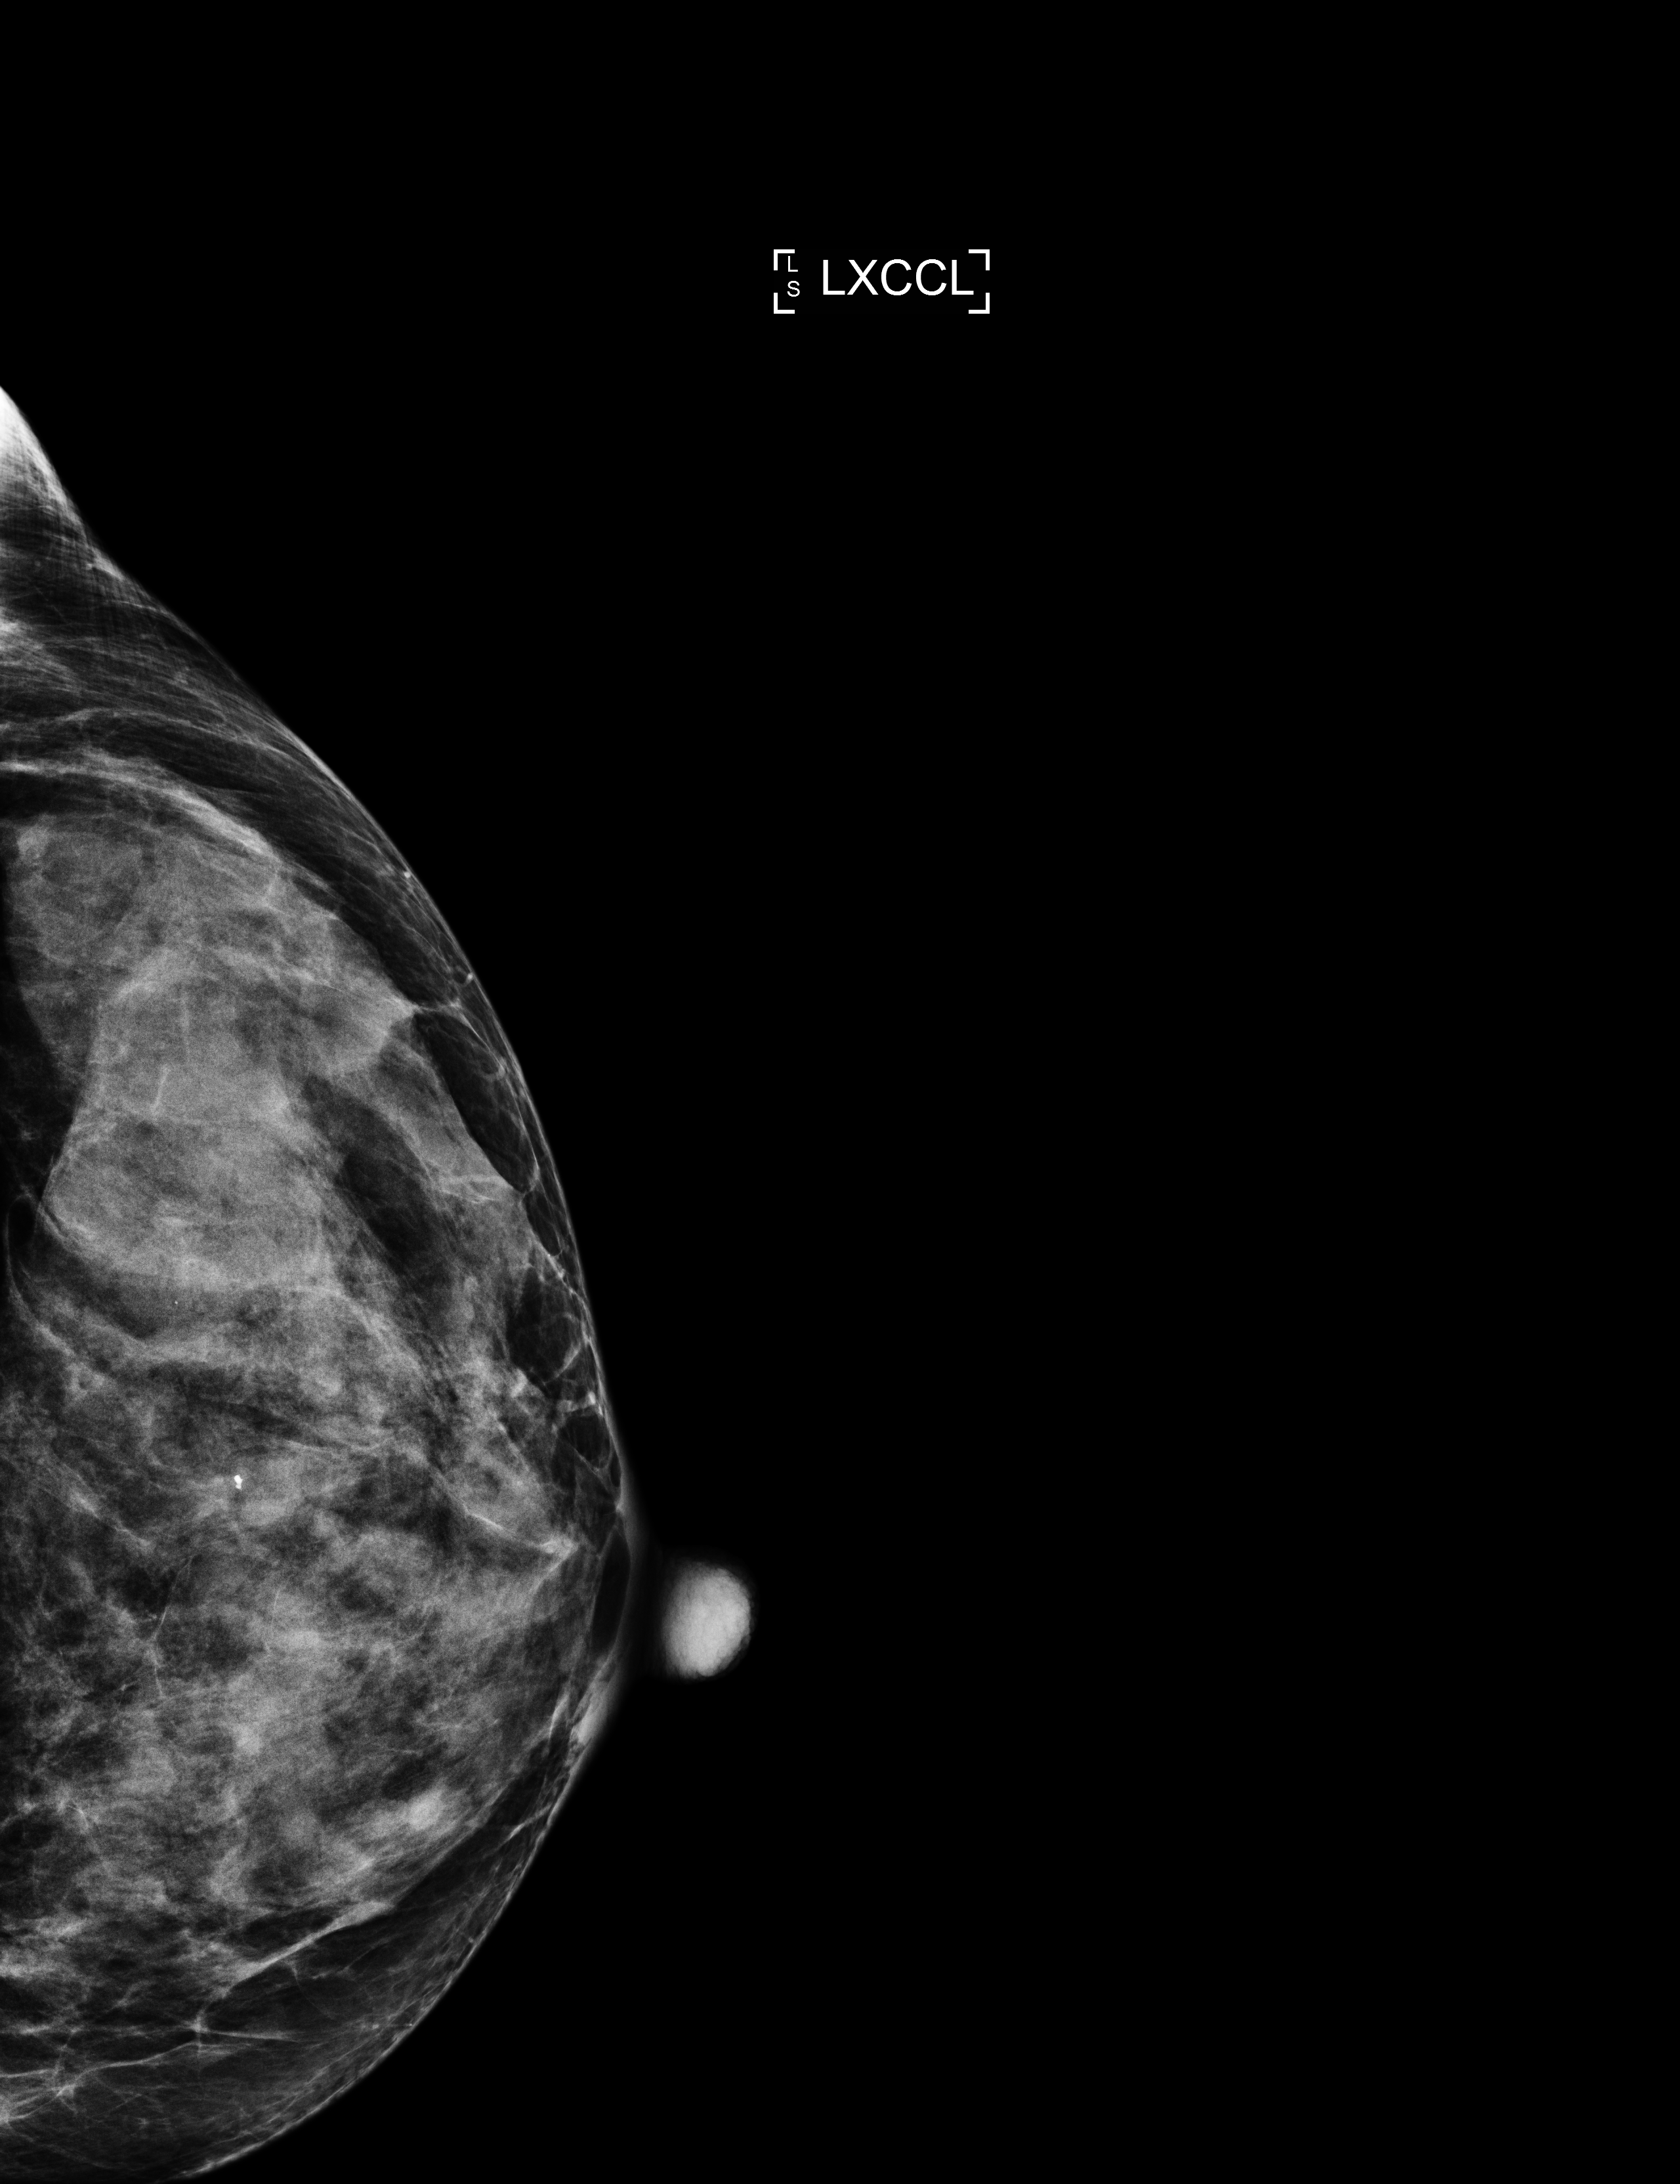
Full-field digital mammogram (FFDM); left breast; laterally exaggerated craniocaudal (XCCL) view; screening examination. Patient: female, 67 years.
Breast density at the screening exam (both breasts): extremely dense (BI-RADS density category d). Final BI-RADS assessment for this screening round (tomosynthesis exam, both breasts): category 2. Recall: no recall after this screen.